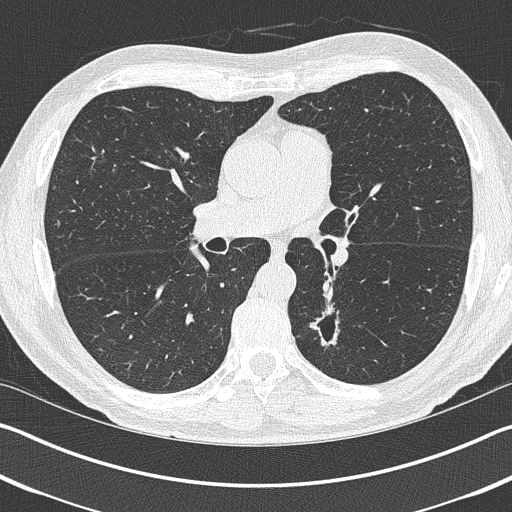
Axial slice from a low-dose chest CT screening exam; baseline annual screen; lung window (W 1500 / L -600 HU); 512 × 512 image matrix. Male, age 69 years at enrolment. Current smoker at enrolment.
Expert-annotated lung lesion, bounding box <296,306,352,362> (left, top, right, bottom; pixels). Reader record for this screening exam (exam-level; its link to the box is not recorded): non-calcified nodule or mass ≥4 mm, left upper lobe, 19 × 19 mm, spiculated (stellate) margins, pre-existing on the prior screen: yes. Official screen result: positive, change unspecified: nodule(s) >= 4 mm or enlarging nodule(s), mass(es), or other non-specific abnormalities suspicious for lung cancer. Participant outcome: lung cancer diagnosed 202 days after this screen — non-small cell carcinoma, left lower lobe, stage IIIA (AJCC 6th edition), 20 mm at pathology.